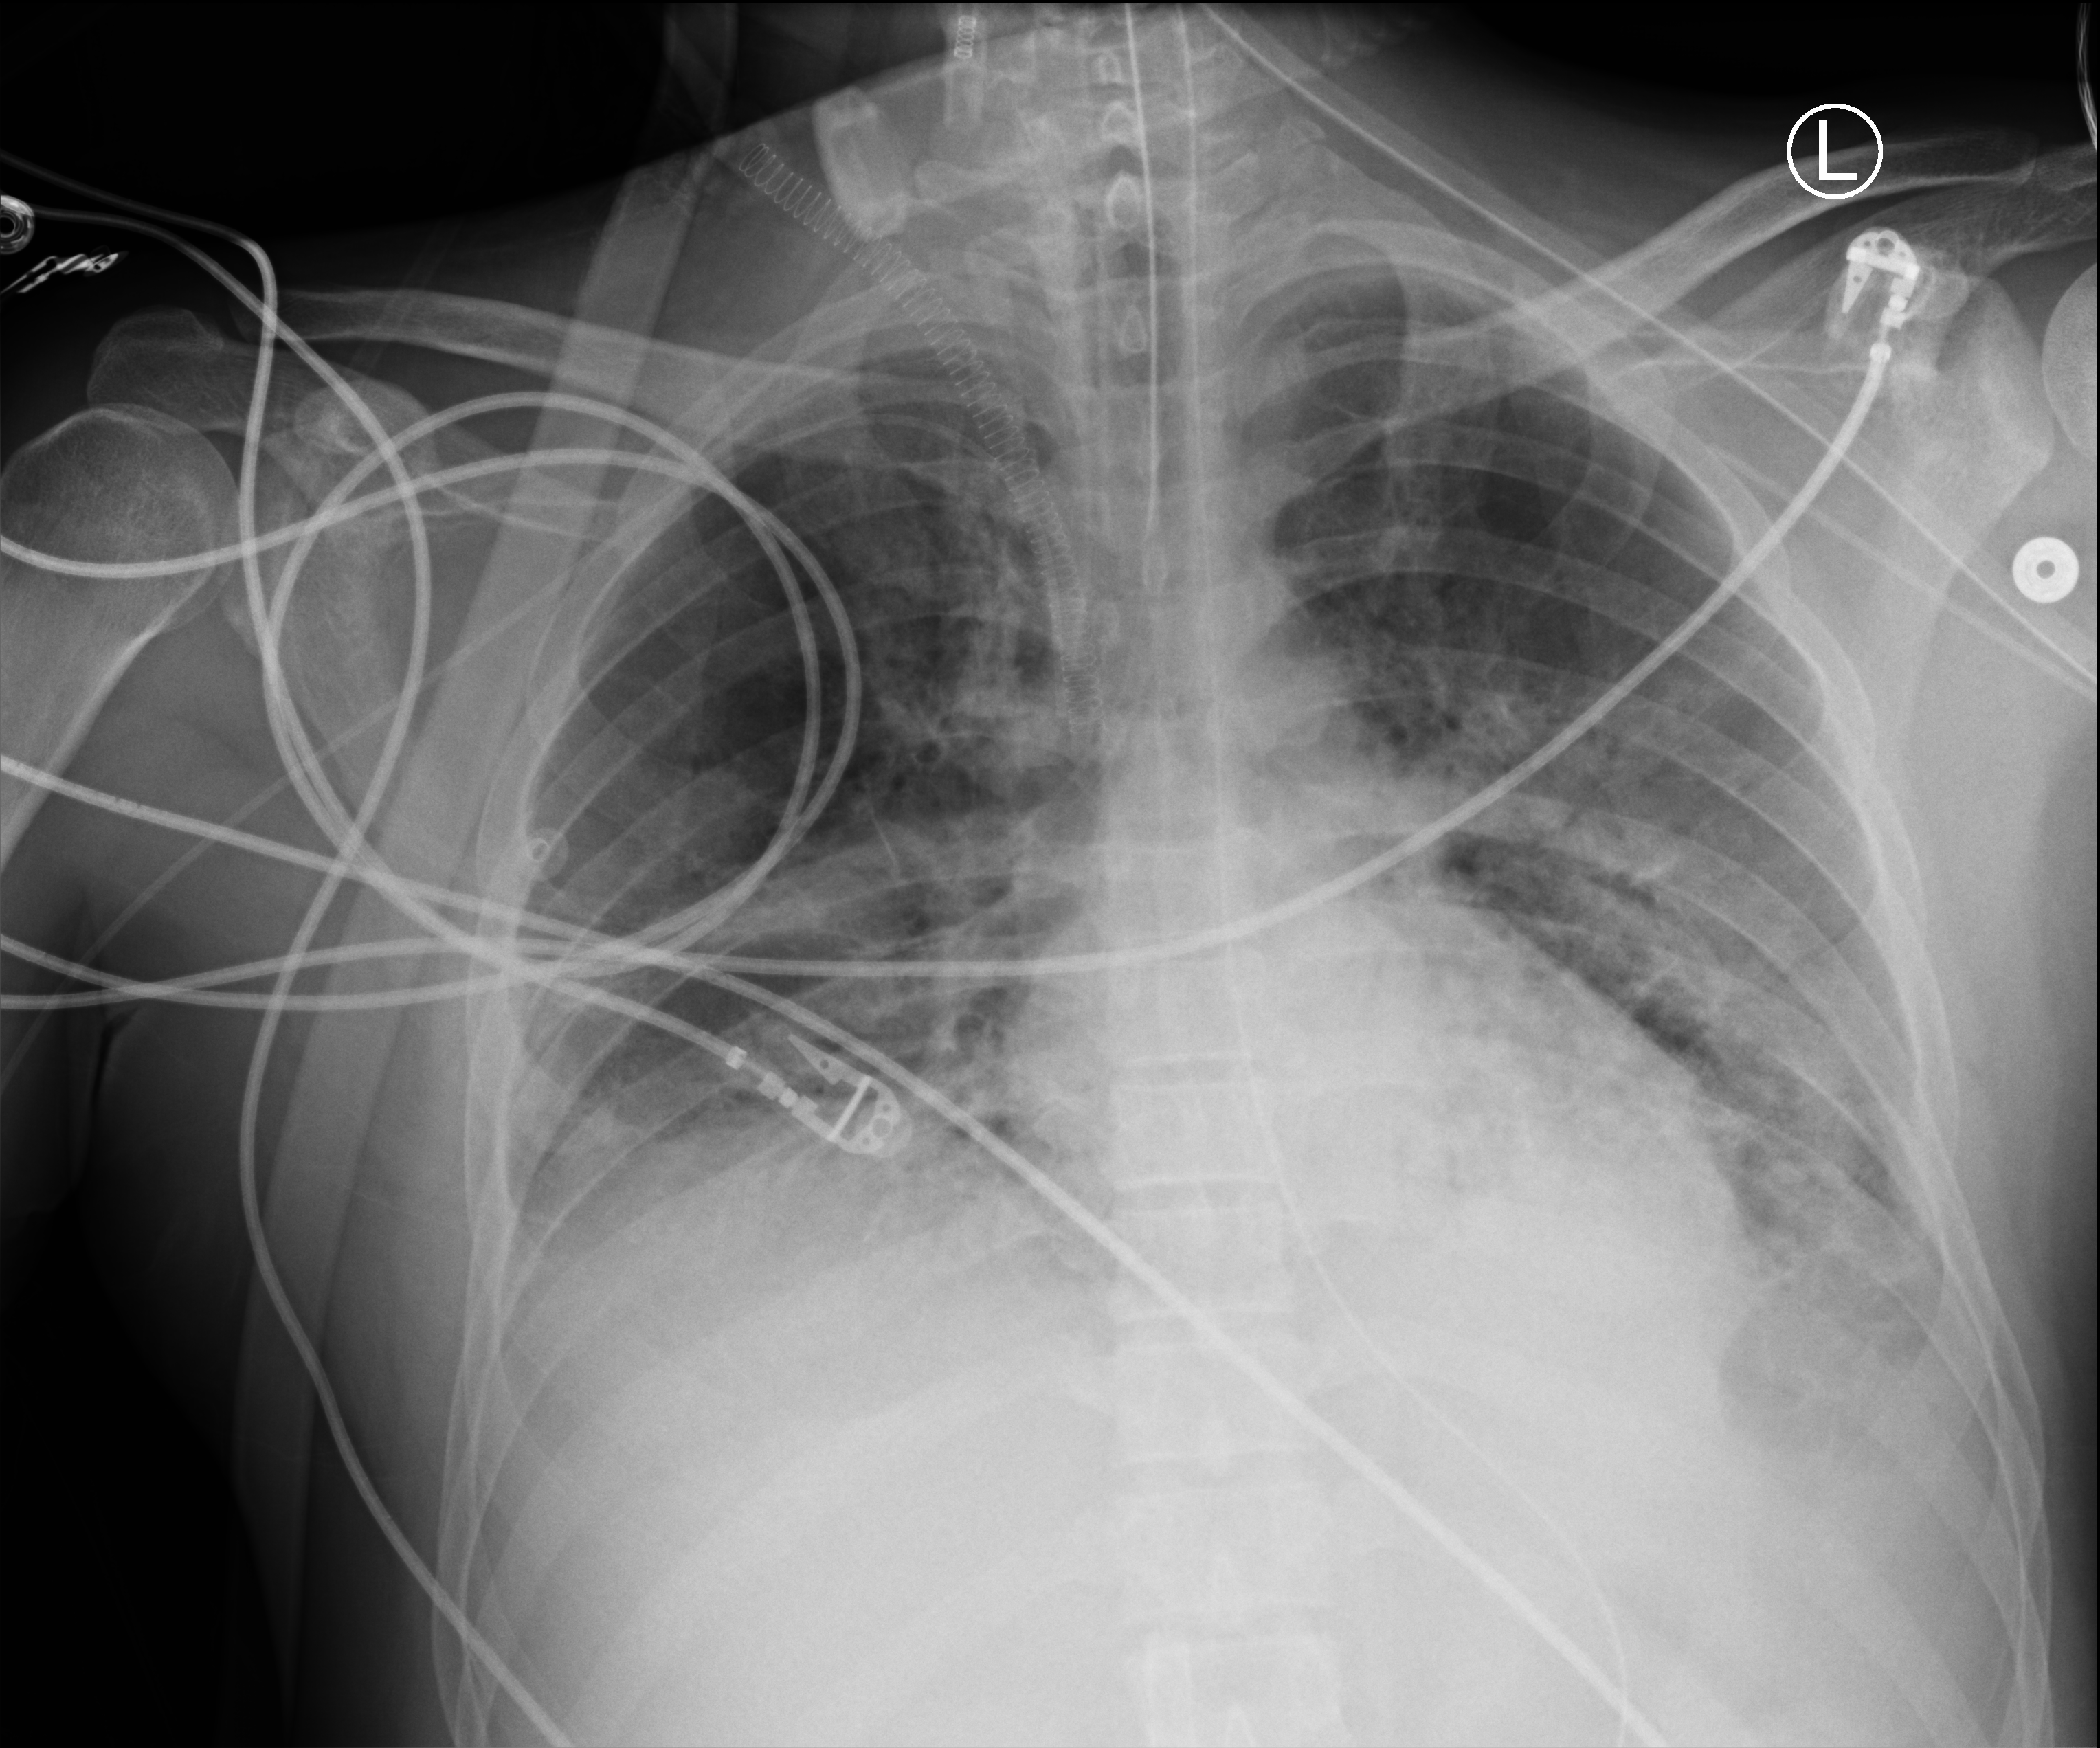
Portable chest radiograph; anteroposterior (AP) projection. Patient hospitalised with COVID-19, aged 18–59 years.
Admission-level facts for this patient (not findings on this image; timing relative to this image not recorded):
- mechanically ventilated during this hospital stay: yes
- admitted to intensive care during this hospital stay: yes